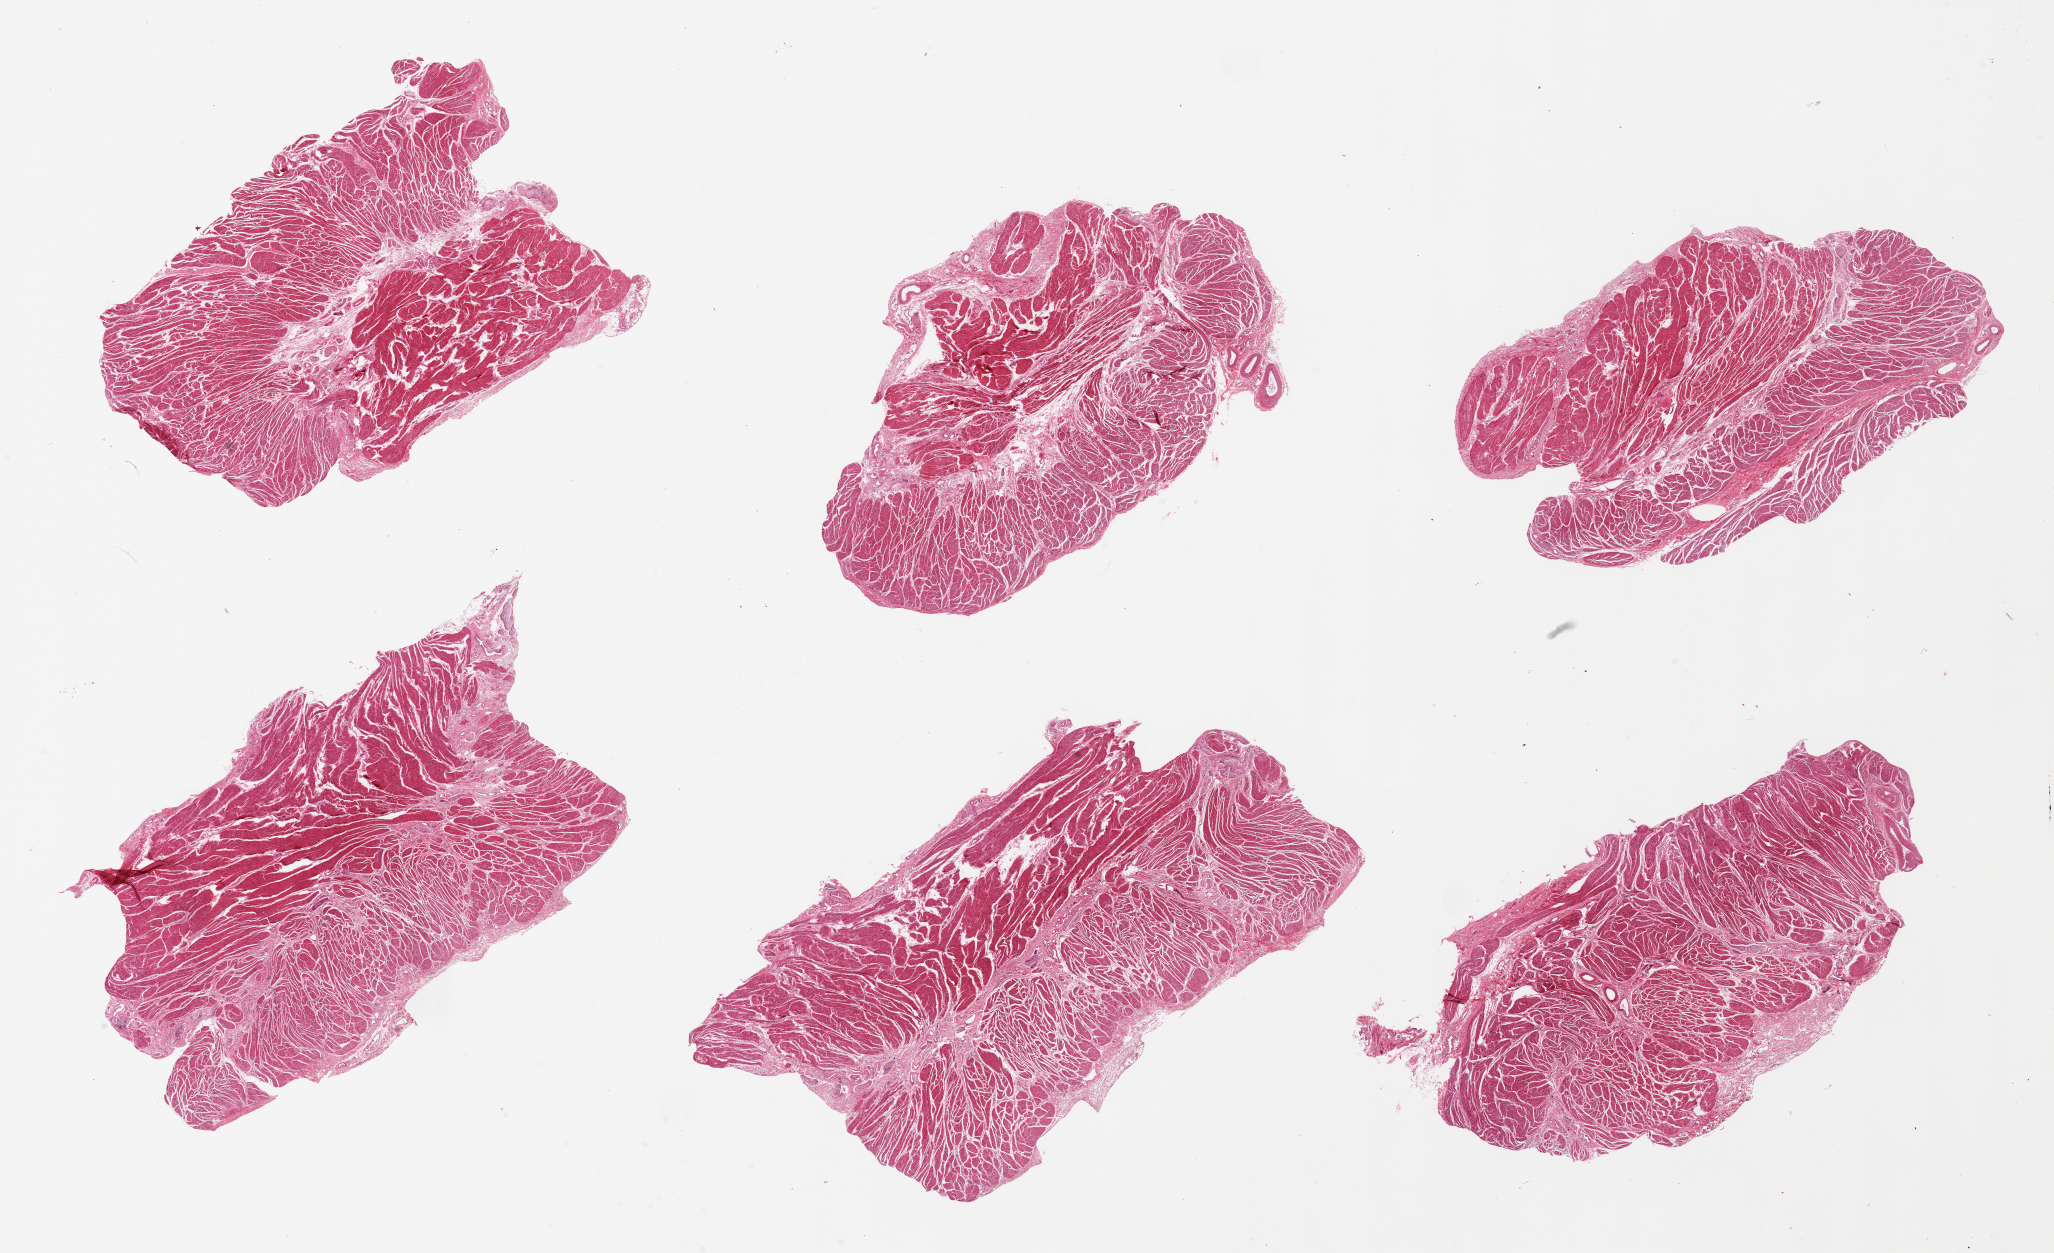
Whole-slide image, hematoxylin and eosin (H&E) stain, brightfield, low-resolution overview of the scanned area, about 32.5 x 19.8 mm, PAXgene-fixed paraffin-embedded (PFPE) section, sampled site (target tissue): gastroesophageal junction, tissue donor sample. Donor sex: male.
Reviewer comment on this tissue sample: 6 pieces. Well dissected.